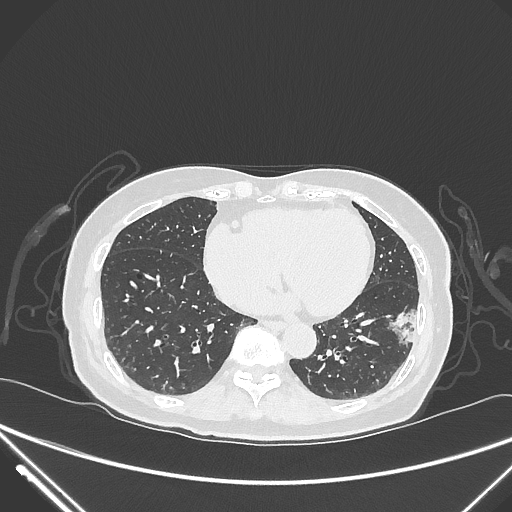
Chest CT, one axial slice; slice 108 of 310 in the series (ordered by position); lung window (W 1500 / L -600 HU); 1 mm slice thickness; 512 × 512 image matrix, field of view 377 × 377 mm. Patient: female, 82 years. From the clinical record (not read from this slice): clinical TNM (as recorded): T1c N0 M0; histopathological grade: G2.
Annotated regions visible in this slice (bounding box drawn by a radiologist):
- lung tumour (recorded histology: adenocarcinoma): bounding box <389,303,421,348> (left, top, right, bottom; pixels)